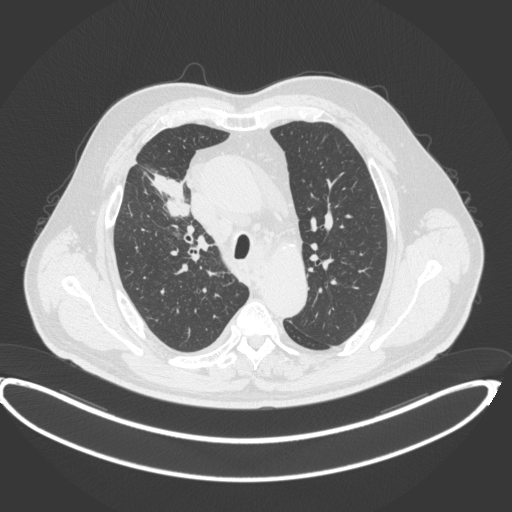
Chest CT, one axial slice. Slice 290 of 395 in the series (ordered by position). Reconstruction kernel B31f. 120 kVp. Lung window (W 1500 / L -600 HU). 512 × 512 image matrix. Patient: male, 62 years. Case-level facts recorded for this patient, not image findings: clinical TNM (as recorded): T1c N3 M1c.
Outlined on this slice (rectangle marked by the reading radiologist):
- lung tumour (recorded histology: adenocarcinoma): bounding box <146,169,193,220> (left, top, right, bottom; pixels)